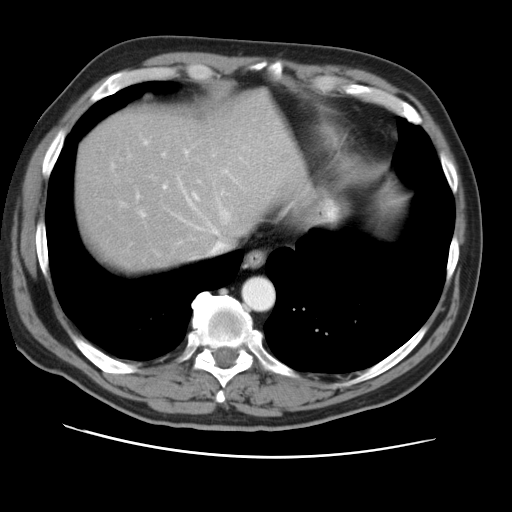
Contrast-enhanced abdominal CT, one axial slice. Position 42 of 49 along the scan axis. 120 kVp. Intravenous contrast given. Soft-tissue window (W 400 / L 40 HU). 5 mm slice thickness. 512 × 512 image matrix, field of view 374 × 374 mm. Male patient, age 59 years. Case-level facts recorded for this patient, not image findings: diagnosis: colorectal cancer liver metastases, imaged before liver resection; multiple liver metastases: yes; largest metastasis: 6.3 cm; disease in both lobes: yes.
Structures marked on this image (expert manual segmentation):
- hepatic veins: bounding box [x1, y1, x2, y2] px = [164, 183, 230, 254]
- liver: [75, 92, 302, 269]
- planned liver remnant (the part of the liver to remain after resection): [75, 92, 299, 269]
- portal vein (with intrahepatic branches): [111, 141, 198, 212]